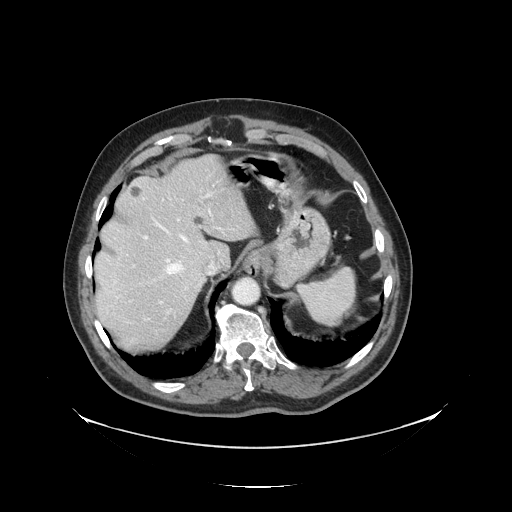
Contrast-enhanced abdominal CT, one axial slice. Slice 106 of 138 in the series (ordered by position). Reconstruction kernel STANDARD. Intravenous contrast given. Soft-tissue window (W 400 / L 40 HU). 512 × 512 image matrix. Male patient, age 77 years. Case-level facts recorded for this patient, not image findings: diagnosis: colorectal cancer liver metastases, imaged before liver resection; multiple liver metastases: no; largest metastasis: 1.5 cm; chemotherapy before resection: no.
Structures marked on this image (outlined manually by an expert reader):
- hepatic veins: bounding box (x1, y1, x2, y2) in pixels: (153, 207, 213, 281)
- liver: (96, 158, 254, 353)
- planned liver remnant (the part of the liver to remain after resection): (95, 158, 255, 290)
- portal vein (with intrahepatic branches): (133, 190, 235, 320)
- liver metastasis: (193, 215, 205, 226)
- liver metastasis: (130, 187, 141, 198)